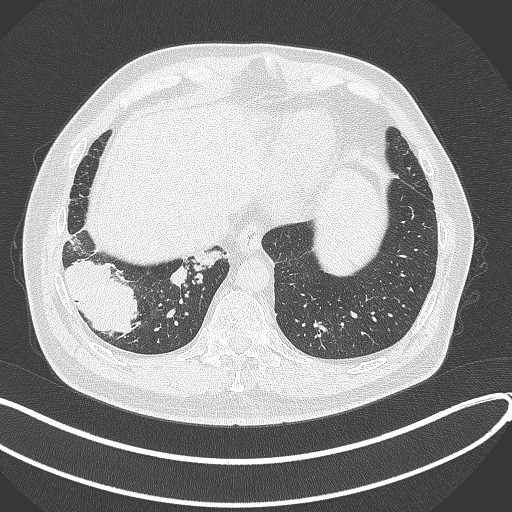
Chest CT, one axial slice. Slice 72 of 360 in the series (ordered by position). Lung window (W 1500 / L -600 HU). 1 mm slice thickness. 512 × 512 image matrix, field of view 400 × 400 mm. Male patient, age 59 years.
Annotated regions visible in this slice (bounding box drawn by a radiologist):
- lung tumour (recorded histology: adenocarcinoma): box from (x=61, y=253) to (x=142, y=339) px